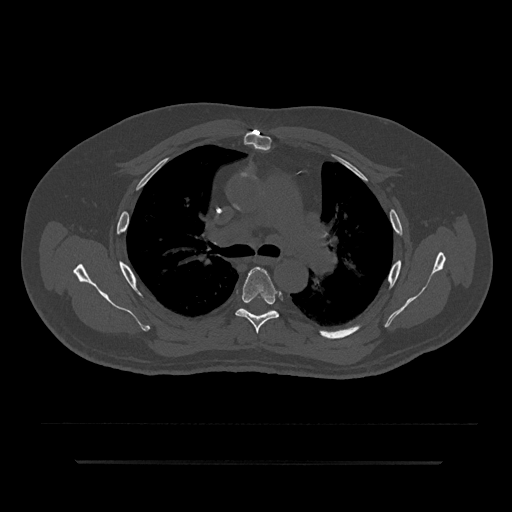
CT including the spine, one axial slice; position 571 of 797 along the scan axis; reconstruction kernel Br40s/3; 120 kVp; bone window (W 1800 / L 400 HU); 0.5 mm slice thickness; 512 × 512 image matrix, field of view 464 × 464 mm. Male patient, age 59 years. Case-level facts recorded for this patient, not image findings: primary cancer: bile ducts.
Annotated regions visible in this slice (semi-automatically segmented with operator editing):
- T5 vertebra: bounding box (x1, y1, x2, y2) in pixels: (235, 267, 279, 334)
- T6 vertebra: (243, 308, 247, 311)